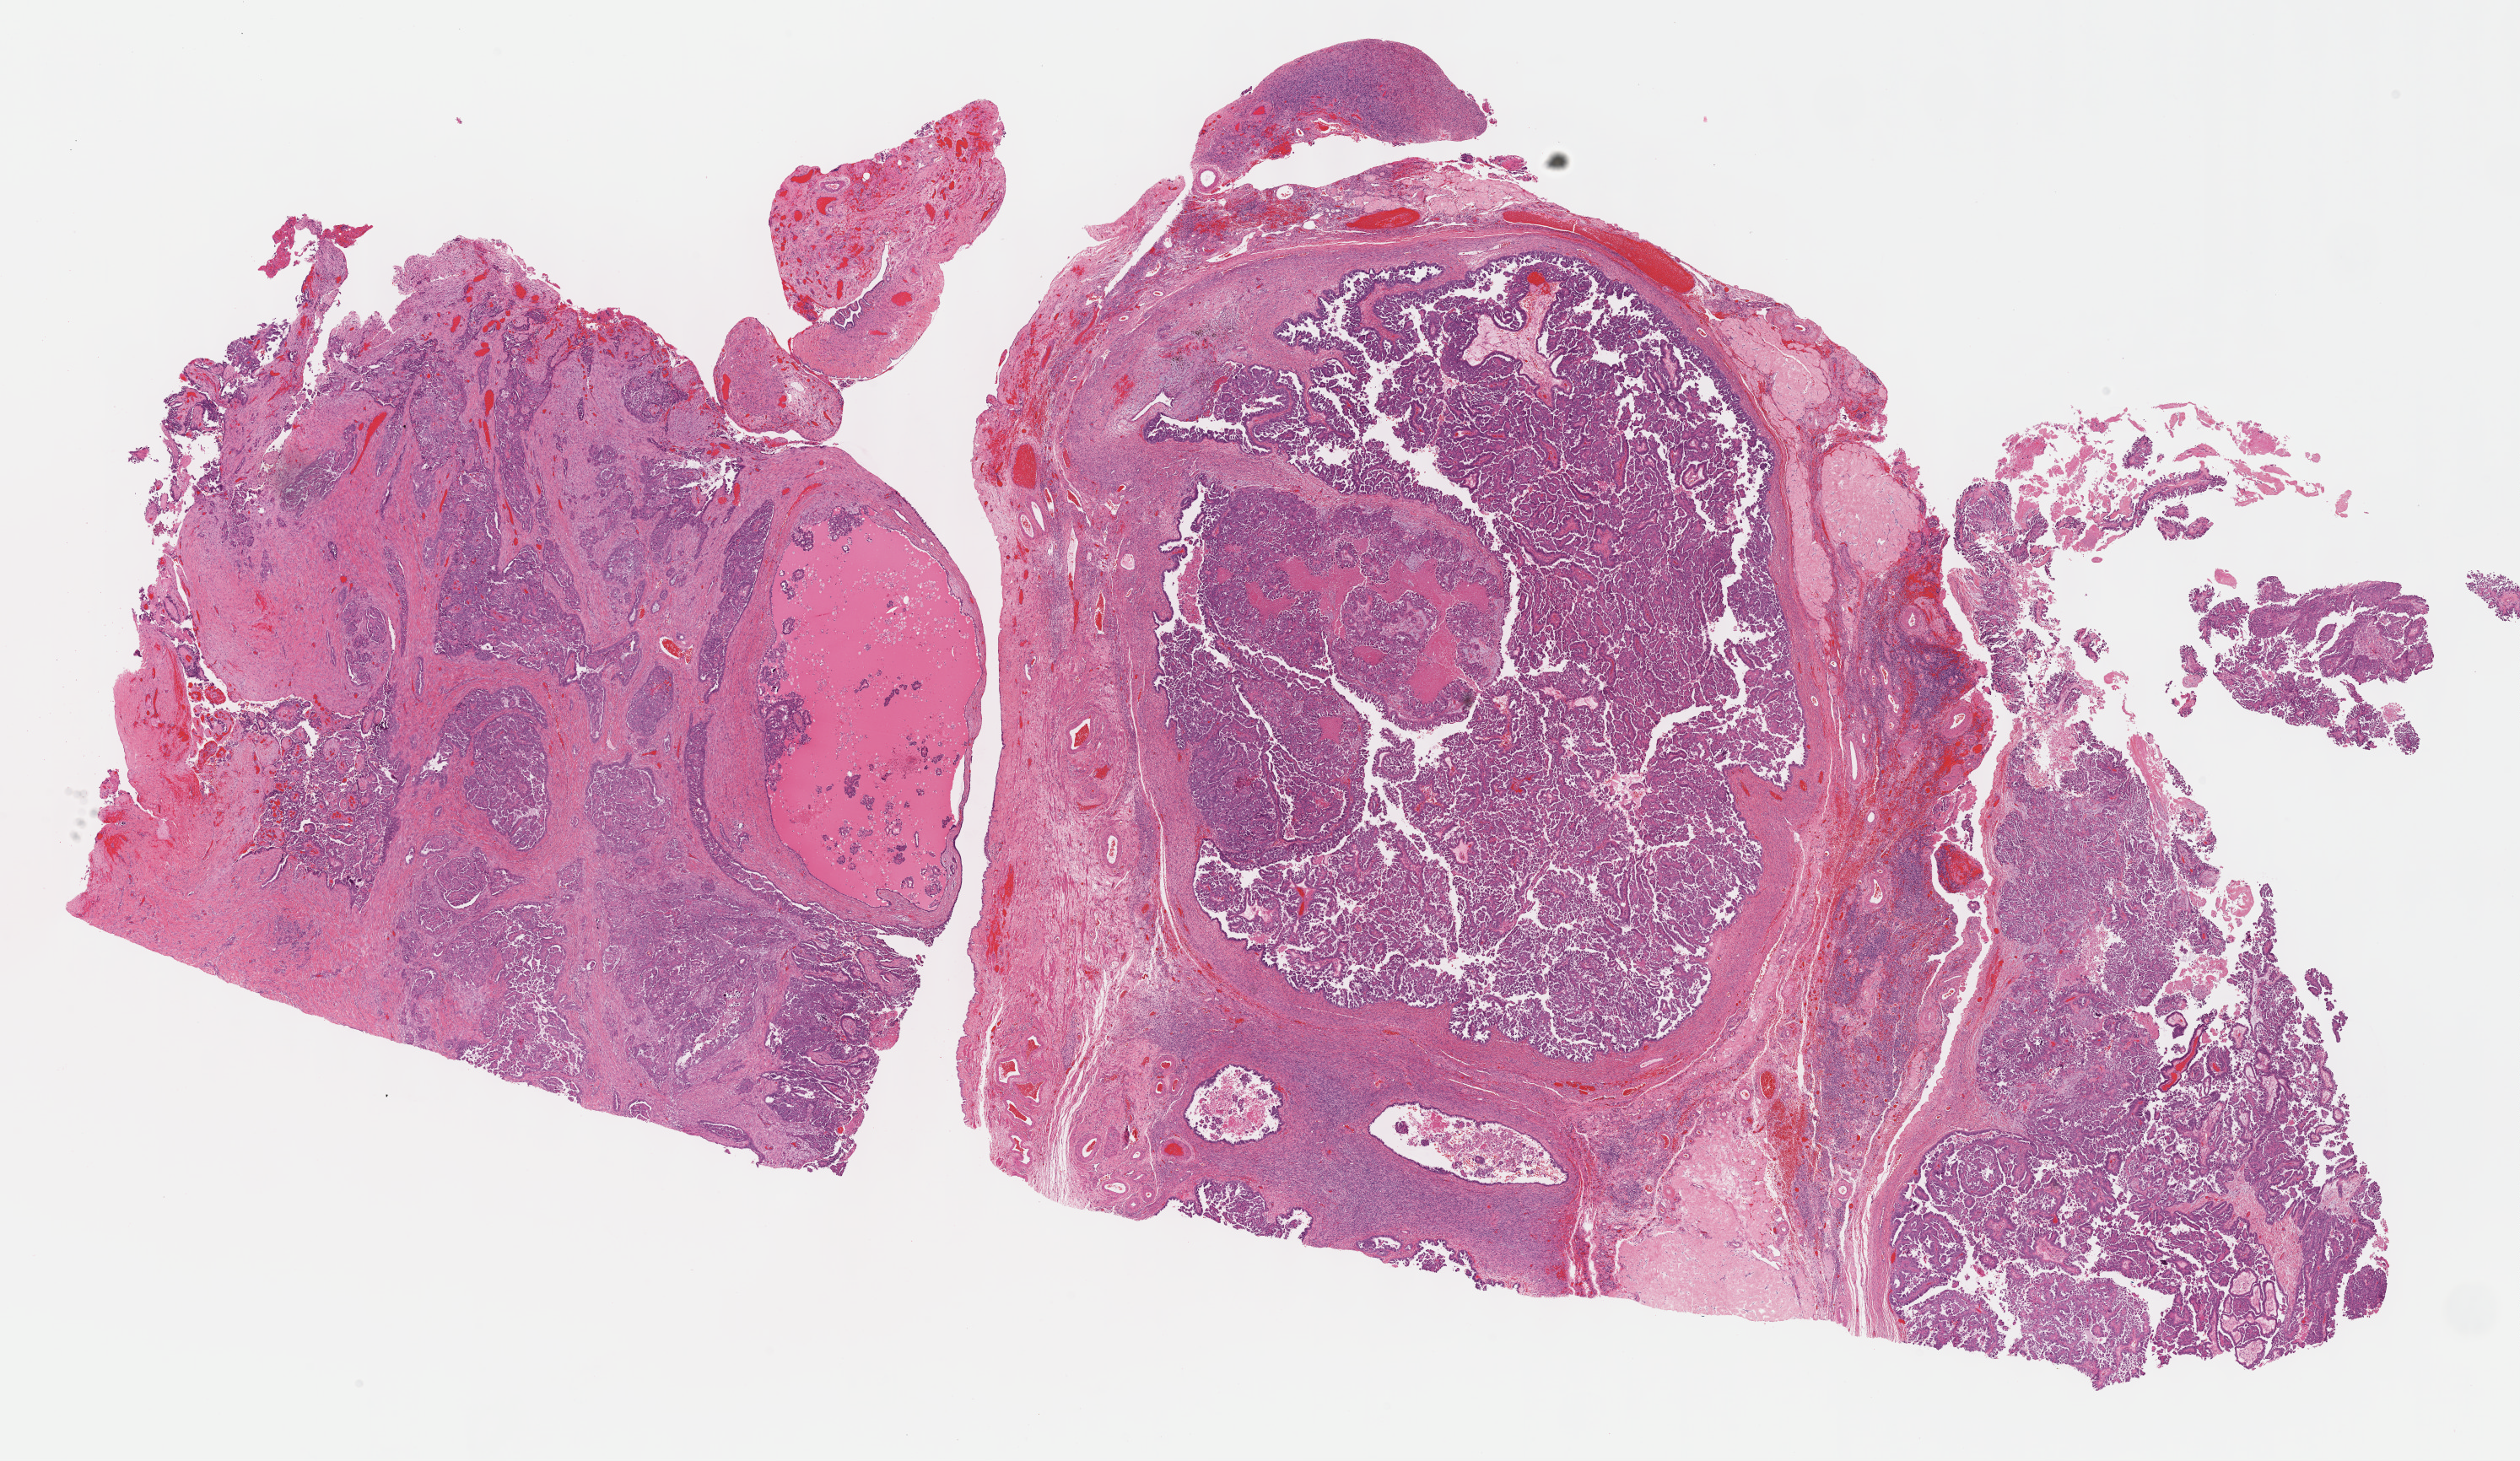
Whole-slide histology image, Hematoxylin and eosin (H&E) stained, a low-resolution overview of the entire scanned area, about 24.2 x 14.0 mm. Formalin-fixed paraffin-embedded (FFPE) diagnostic section. Ovary, primary tumour sample. Female patient; age at initial diagnosis 63 years. Histologic grade: G3 (poorly differentiated).
- FIGO stage: IIIC
- laterality: right
- histologic diagnosis: Serous cystadenocarcinoma, NOS